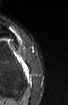
MRI of an extremity soft-tissue mass, one axial slice; position 19 of 52 along the scan axis; STIR; MR volume resampled by the dataset authors to the PET/CT grid (not the native acquisition matrix); 3.27 mm slice thickness; 68 × 105 image matrix, field of view 66 × 103 mm. Female patient. From the clinical record (not read from this slice): histological type: spindle cell suggestive of biphasic synovial sarcoma; grade: intermediate; site of the primary tumour: left knee.
Structures marked on this image (expert contour drawn on MRI and transferred to this co-registered scan by the dataset authors):
- gross tumour volume including surrounding oedema: bounding box (x1, y1, x2, y2) in pixels: (19, 59, 29, 73)